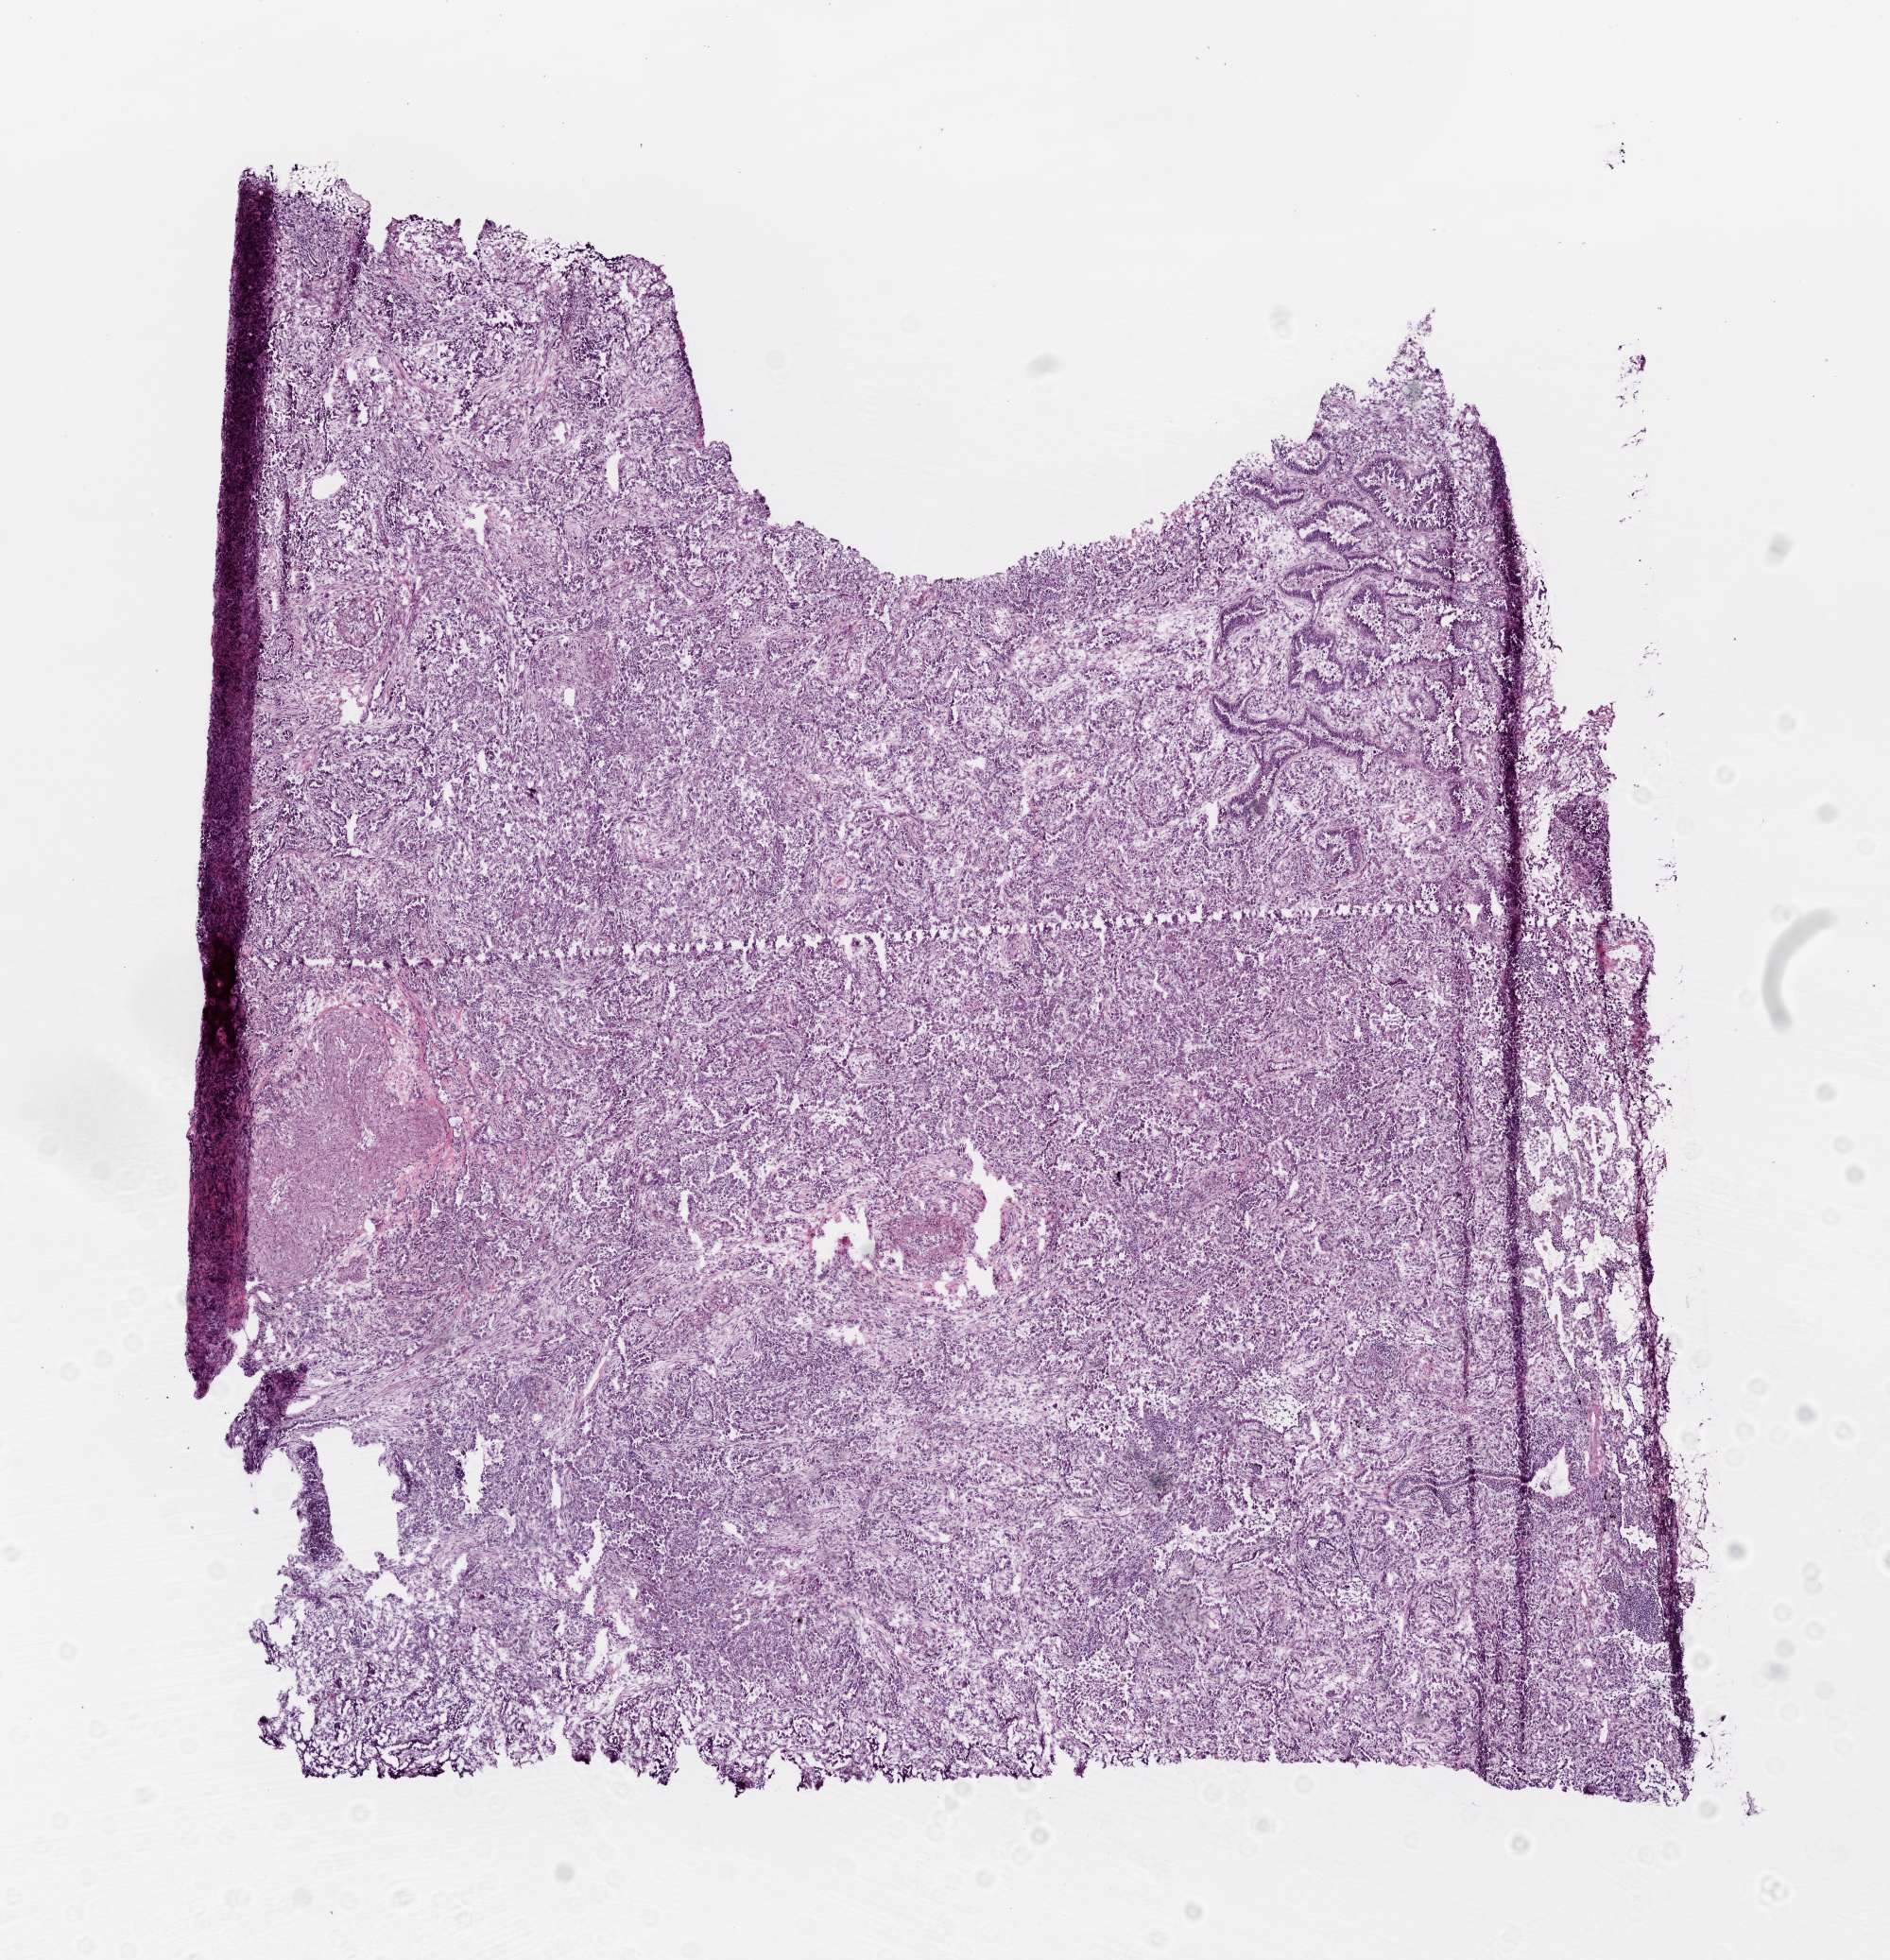
Digitized H&E-stained tissue section (whole slide) — low-resolution overview of the scanned area, about 8.0 x 8.3 mm (slide scanned at 20x). Frozen section. Primary tumour sample from the lung. Female patient; age at initial diagnosis 74 years. Slide review estimates, as recorded: tumour cells 78%, tumour nuclei 70%, normal cells 2%, stromal cells 20%, necrosis 0%.
Diagnosis: Adenocarcinoma with mixed subtypes (lower lobe, lung). AJCC pathologic stage: IB (5th edition).